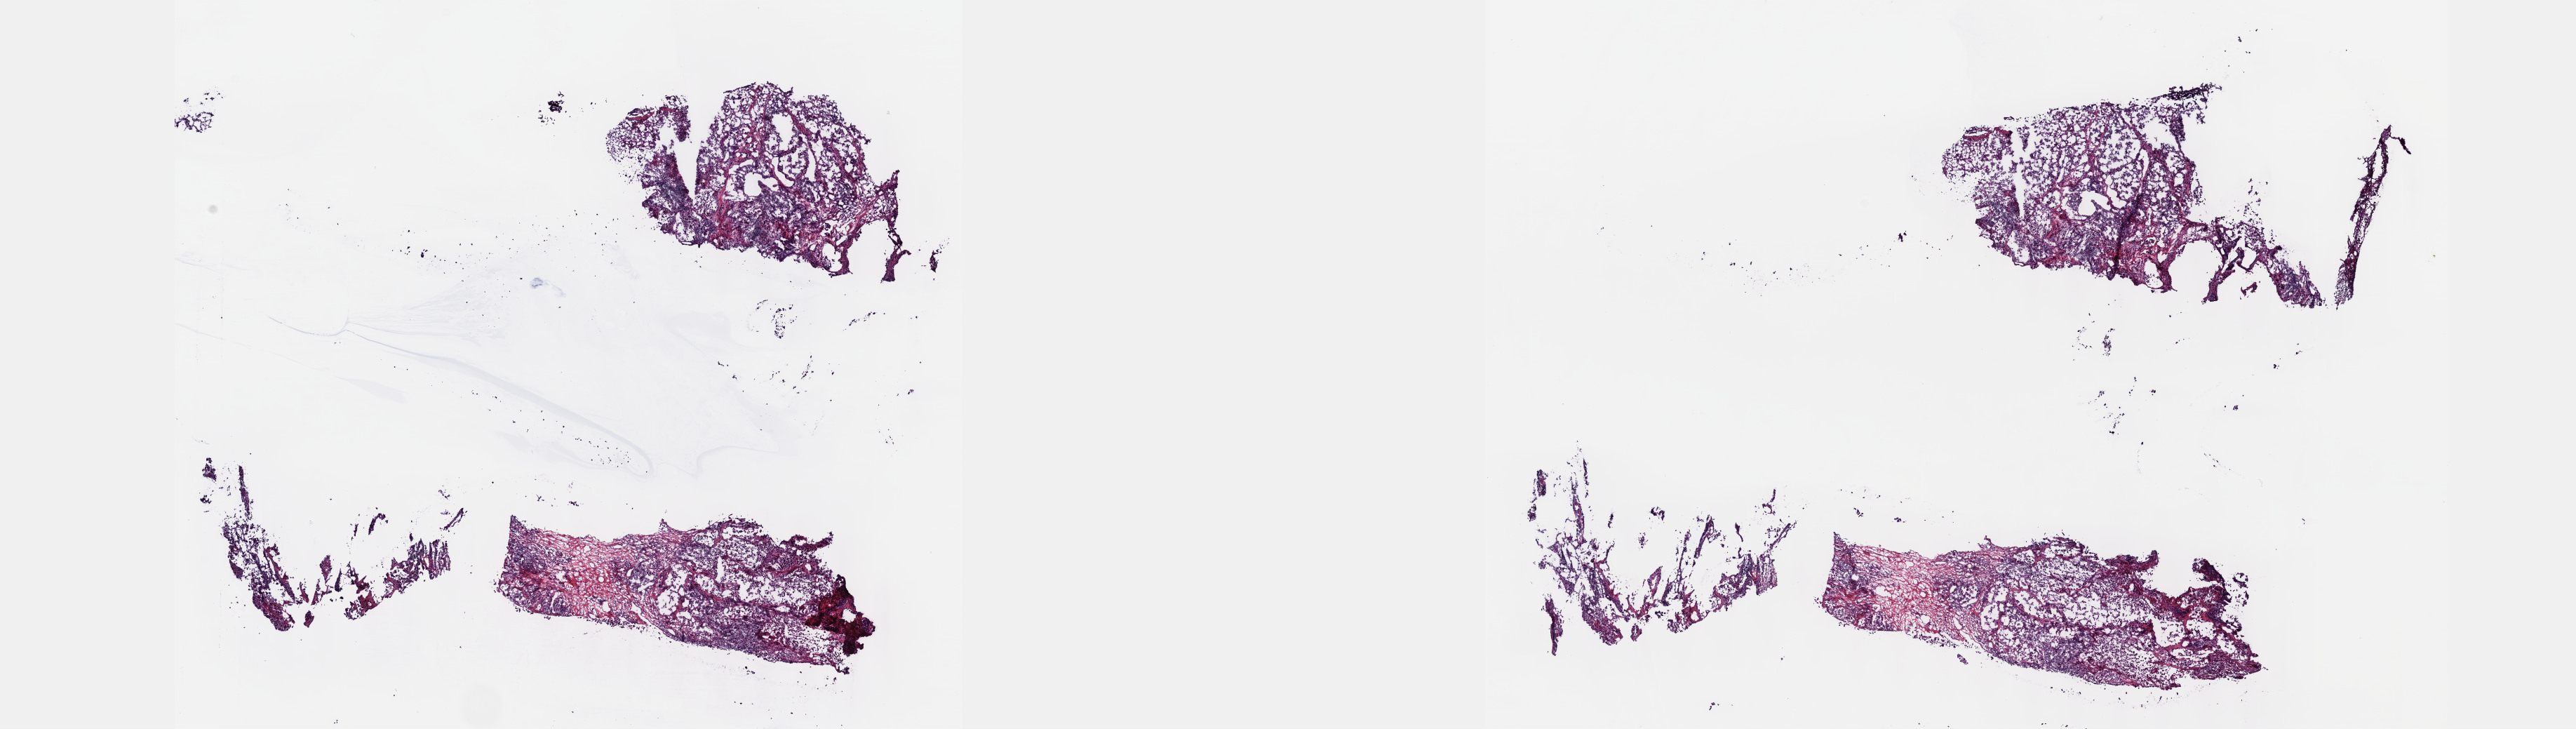
Digitized H&E-stained tissue section (whole slide), a low-resolution overview of the entire scanned area, about 29.7 x 8.4 mm. Frozen section from the top of the tissue portion. Metastatic tumour sample, sampled site not recorded. Female patient. Composition of this section per pathologist review: tumour cells 100%, tumour nuclei 65%.
This section: metastatic tumour tissue. Patient diagnosis: Malignant melanoma, NOS.